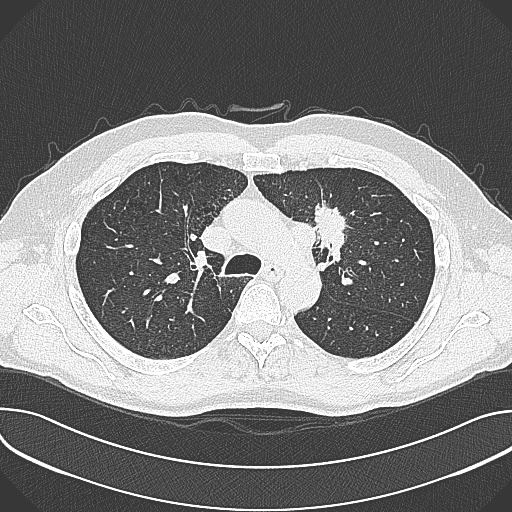
Chest CT (low-dose screening protocol), one axial image; baseline annual screen; lung window (W 1500 / L -600 HU); 1 mm slice thickness; 512 × 512 image matrix. Male participant, aged 59 years at enrolment. Current smoker at enrolment.
Expert-annotated lung lesion, bounding box [x1, y1, x2, y2] px = [302, 197, 361, 257]. The screening reader recorded 2 non-calcified nodules or masses ≥4 mm on this exam (left upper lobe, left upper lobe); which of them this box marks is not recorded. Official screen result: positive, change unspecified: nodule(s) >= 4 mm or enlarging nodule(s), mass(es), or other non-specific abnormalities suspicious for lung cancer. Participant outcome: lung cancer diagnosed 21 days after this screen — non-small cell carcinoma, left upper lobe, poorly differentiated (G3), stage IIIA (AJCC 6th edition), 35 mm at pathology.